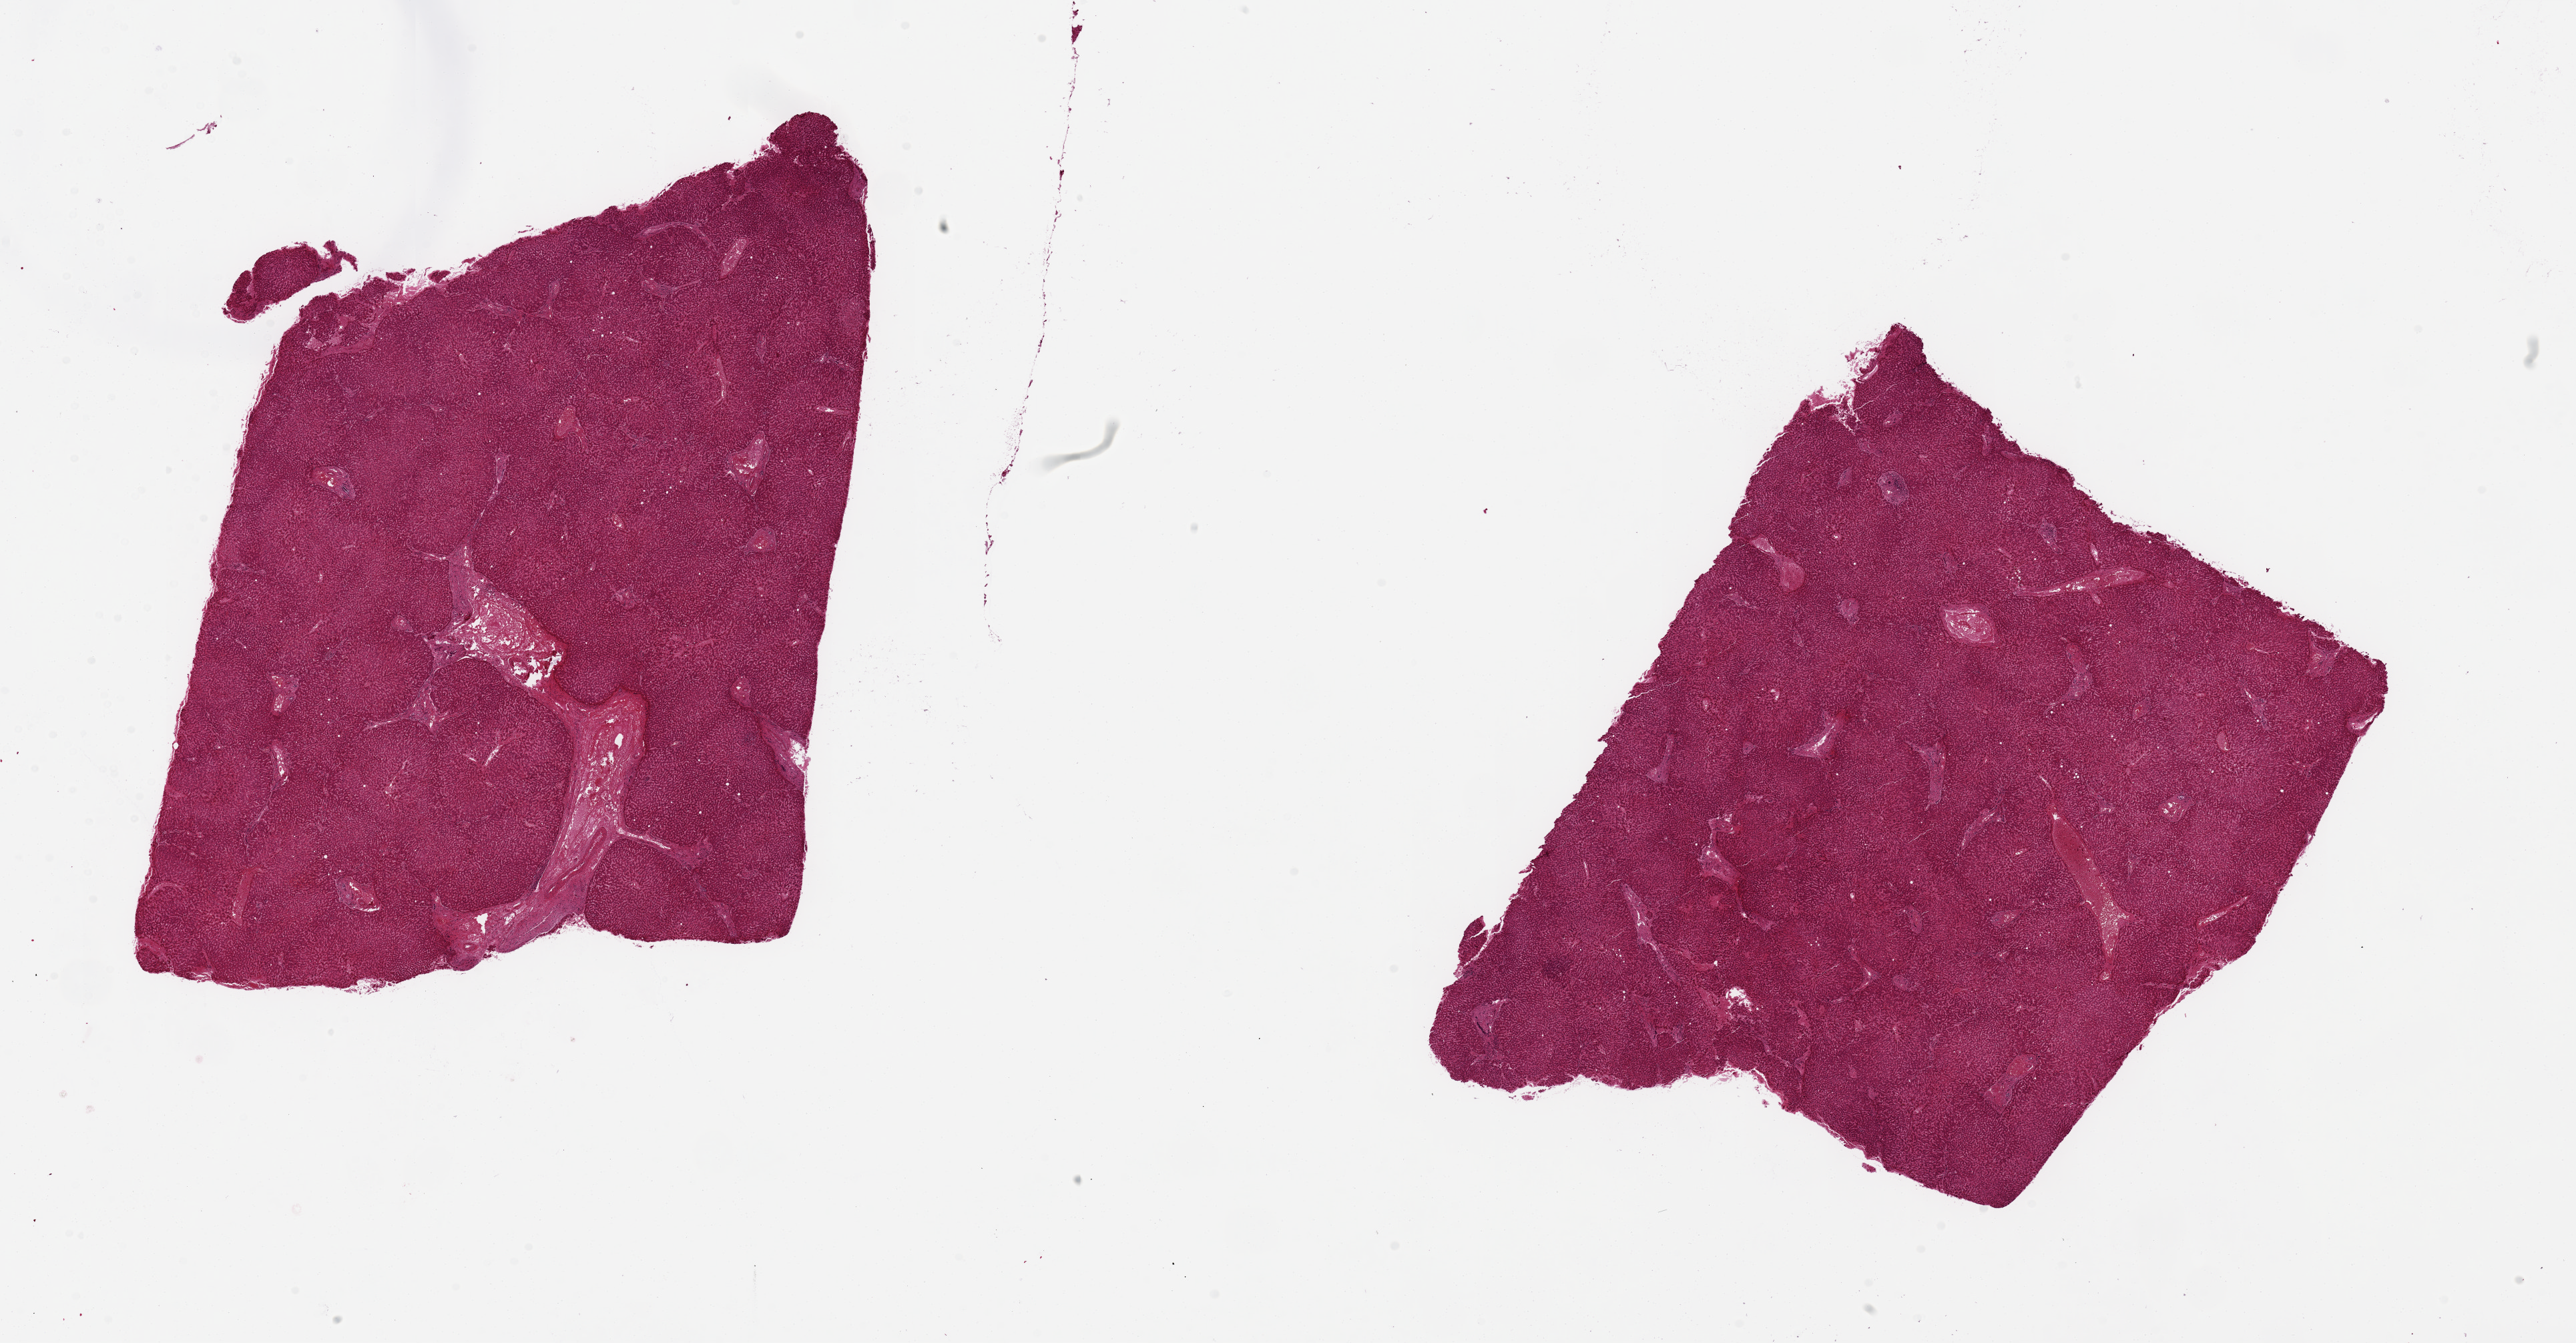
Digitized hematoxylin and eosin (H&E)-stained section — shown as a low-resolution overview of the whole scanned area (about 30.5 x 15.9 mm); PAXgene-fixed, paraffin-embedded tissue; section of liver (target tissue); donor tissue sample. Donor sex: male.
Pathologist's review note for this sample: 2 pieces ~10x8mm. Moderate congestion, moderately autolyzed.